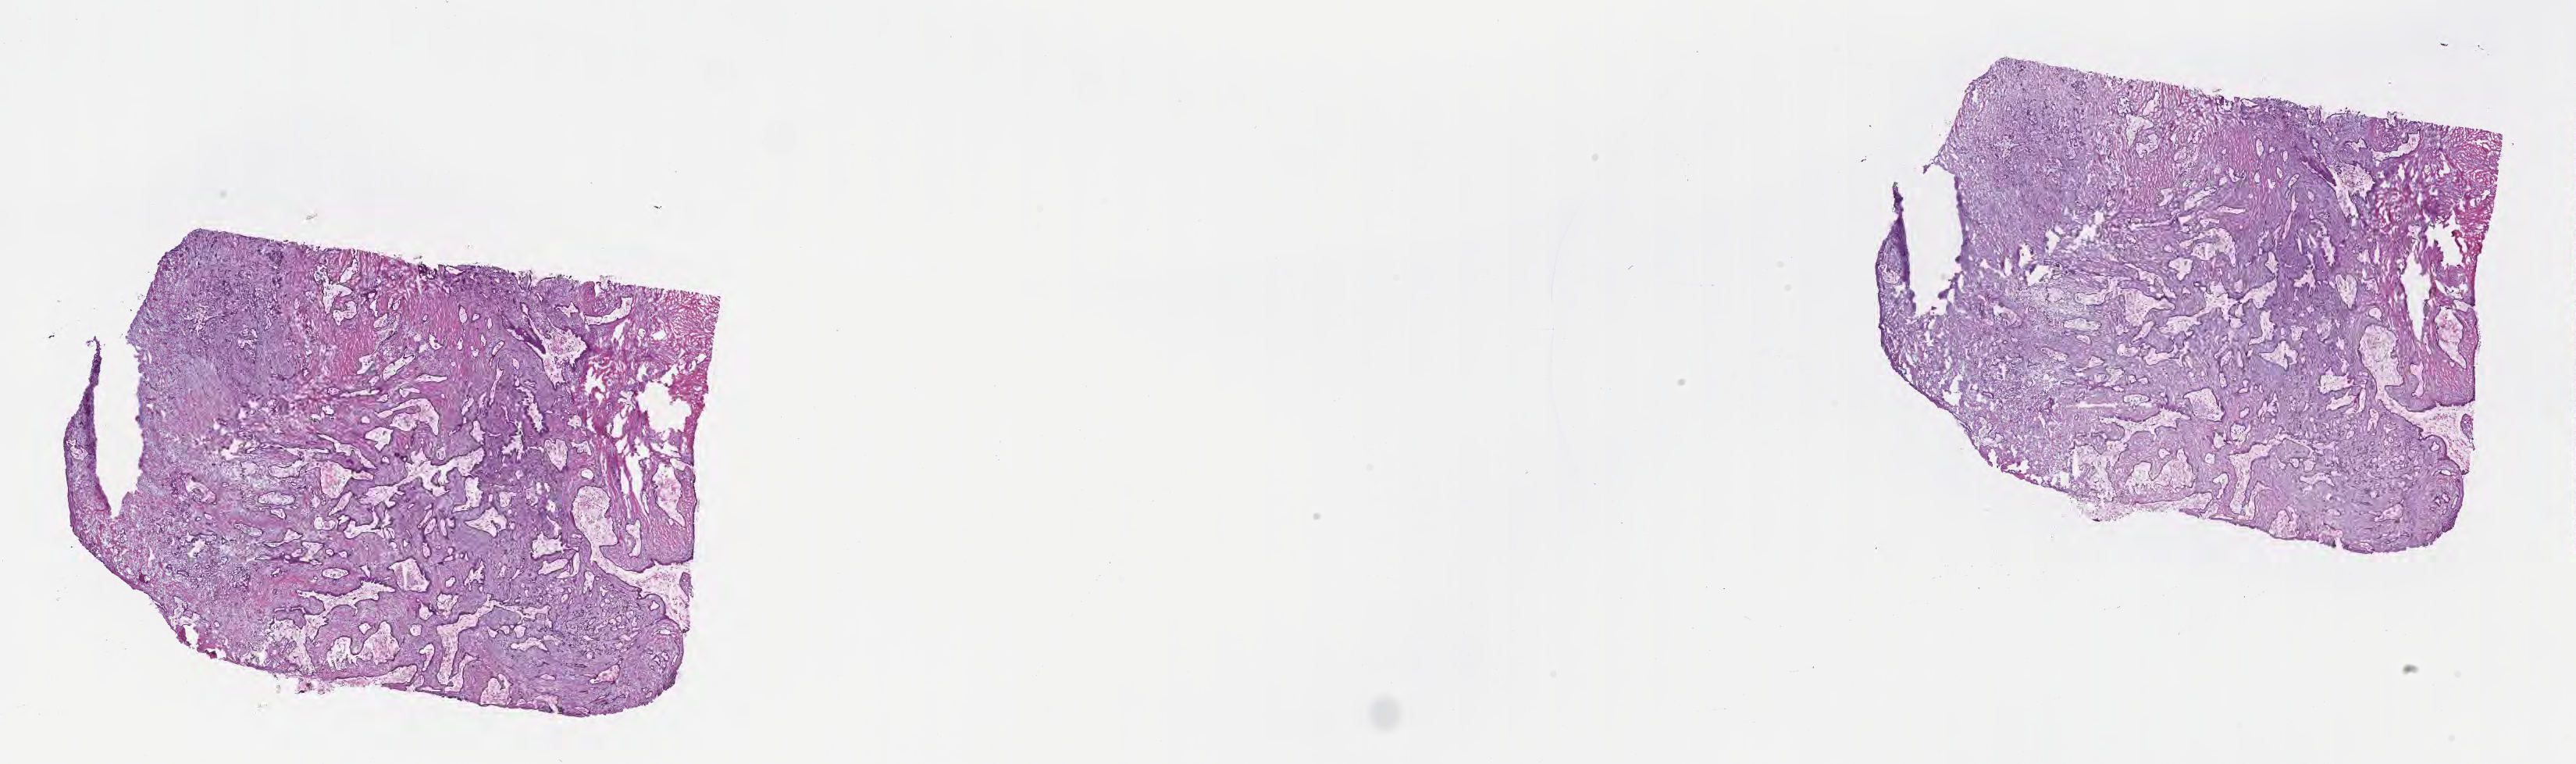
Digitized haematoxylin and eosin-stained section, a low-resolution overview of the entire scanned area, about 26.7 x 7.9 mm, cryosection, specimen: primary tumor, anatomic site: tail of pancreas. Male patient; age at initial diagnosis 63 years.
Diagnosis: Infiltrating duct carcinoma, NOS.